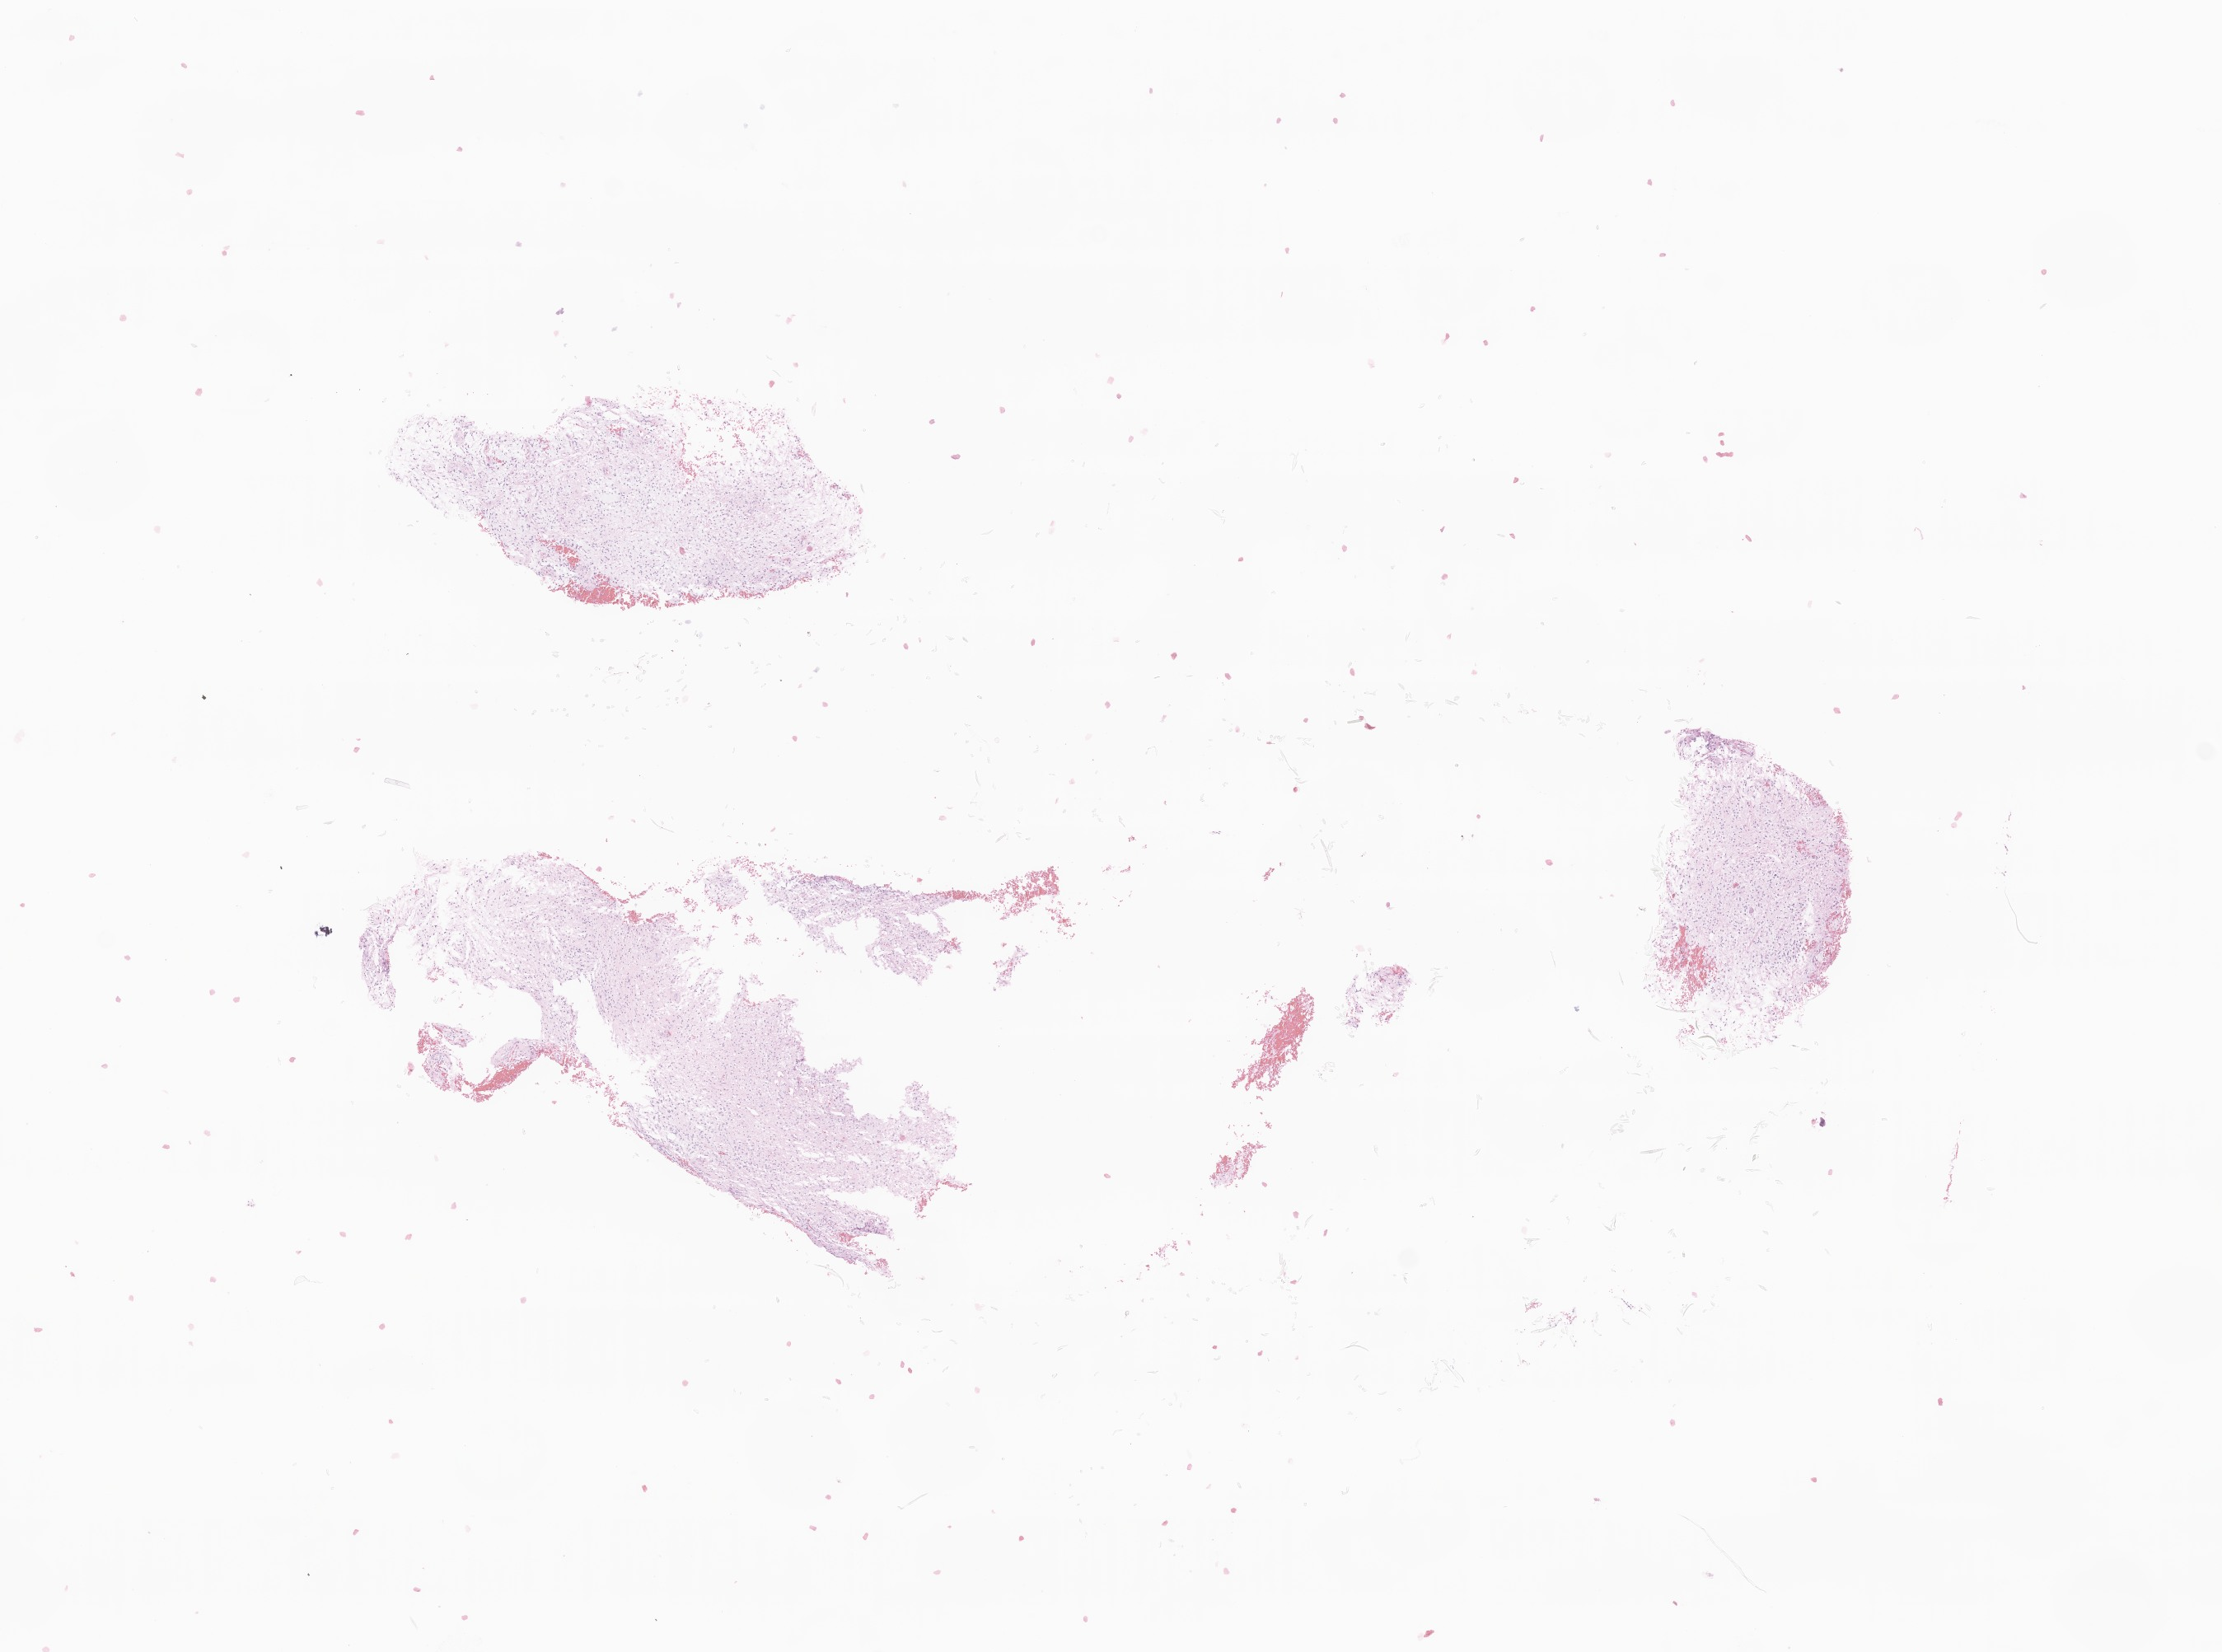
Whole-slide image, hematoxylin and eosin (H&E) stain of tumor tissue from the spinal cord — low-resolution overview of the scanned area, about 11.4 x 8.5 mm, formalin-fixed paraffin-embedded section. Patient female; age 159 months (13 years 3 months).
• recorded diagnosis: Pilocytic astrocytoma